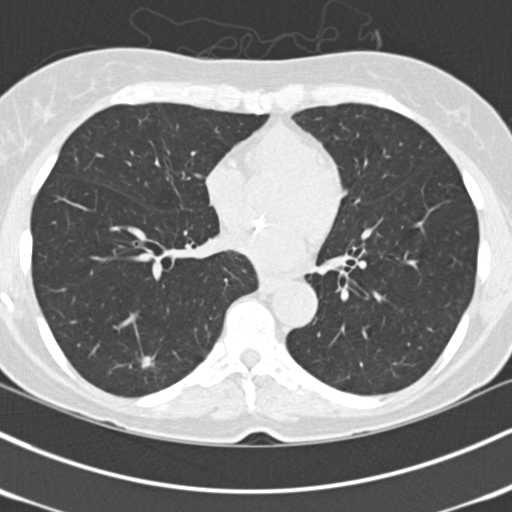
Low-dose screening chest CT, one axial slice. Slice 61 of 150 in the series (ordered by position). Lung window (W 1500 / L -600 HU). 512 × 512 image matrix.
Structures marked on this image (outlined manually by an expert reader):
- lesion 1 (tumor): bounding box [x1, y1, x2, y2] px = [142, 356, 153, 368]